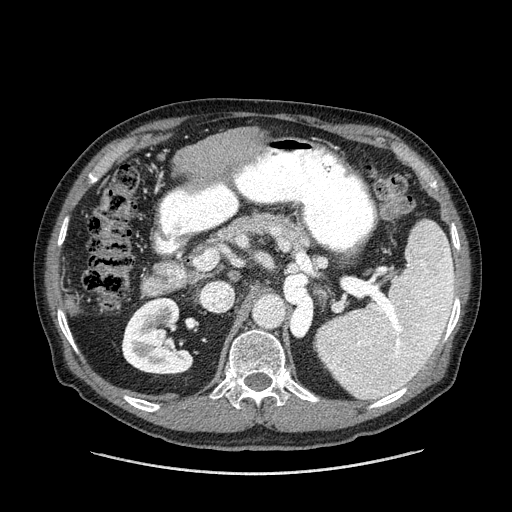
Contrast-enhanced abdominal CT (liver protocol), one axial slice. Slice 64 of 180 in the series (ordered by position). One of 2 acquisitions stored at this slice position. Soft-tissue window (W 400 / L 40 HU). 2.5 mm slice thickness. 512 × 512 image matrix, field of view 420 × 420 mm. From the clinical record (not read from this slice): diagnosis: hepatocellular carcinoma (patient treated with transarterial chemoembolisation; whether this scan precedes or follows treatment is not stated here); TNM stage (as recorded): Stage-II; Child-Pugh class: A; tumour nodularity: multinodular.
Annotated regions visible in this slice (semi-automatically segmented with operator editing):
- liver parenchyma outside the tumour (the mass and vessels are separate outlines, so this box may not span the whole liver): box from (x=66, y=130) to (x=246, y=314) px